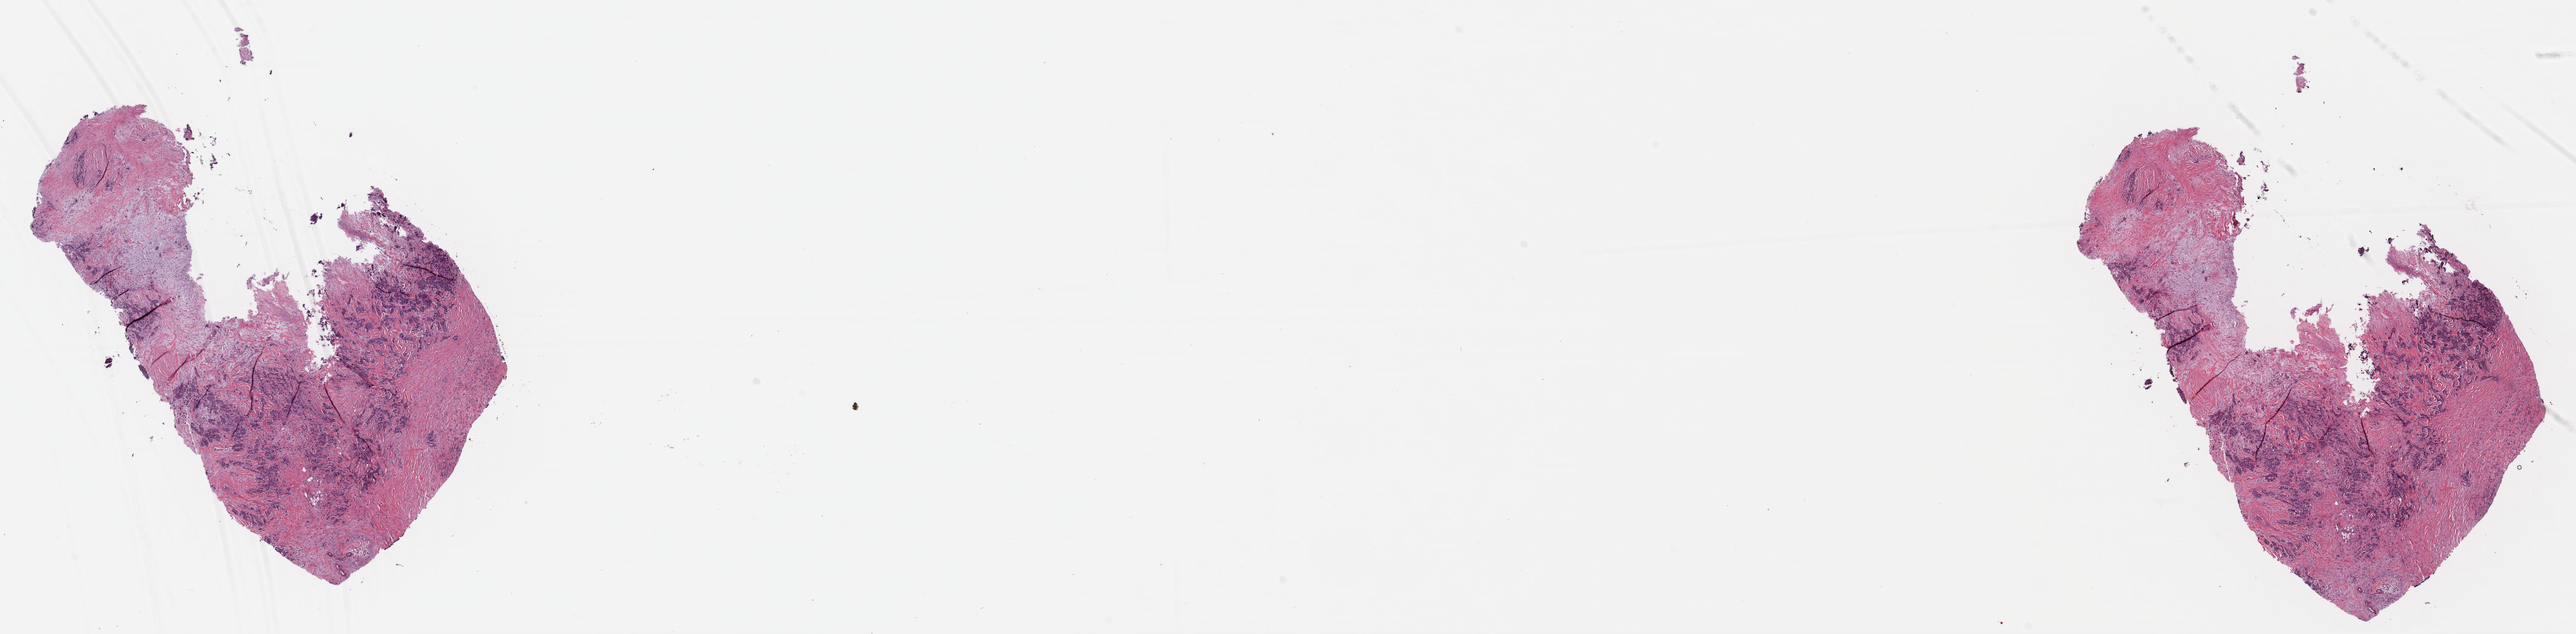
Digitized H&E tissue section (whole slide) — whole scanned area (about 26.7 x 6.6 mm) shown as a low-resolution overview, formalin-fixed paraffin-embedded (FFPE) diagnostic section, sample: primary tumour, breast. Female, age 37 years at initial diagnosis.
AJCC pathologic stage: IIA. Pathologic diagnosis: Infiltrating duct carcinoma, NOS. Lymph nodes positive (case pathology): 0 of 1 examined.